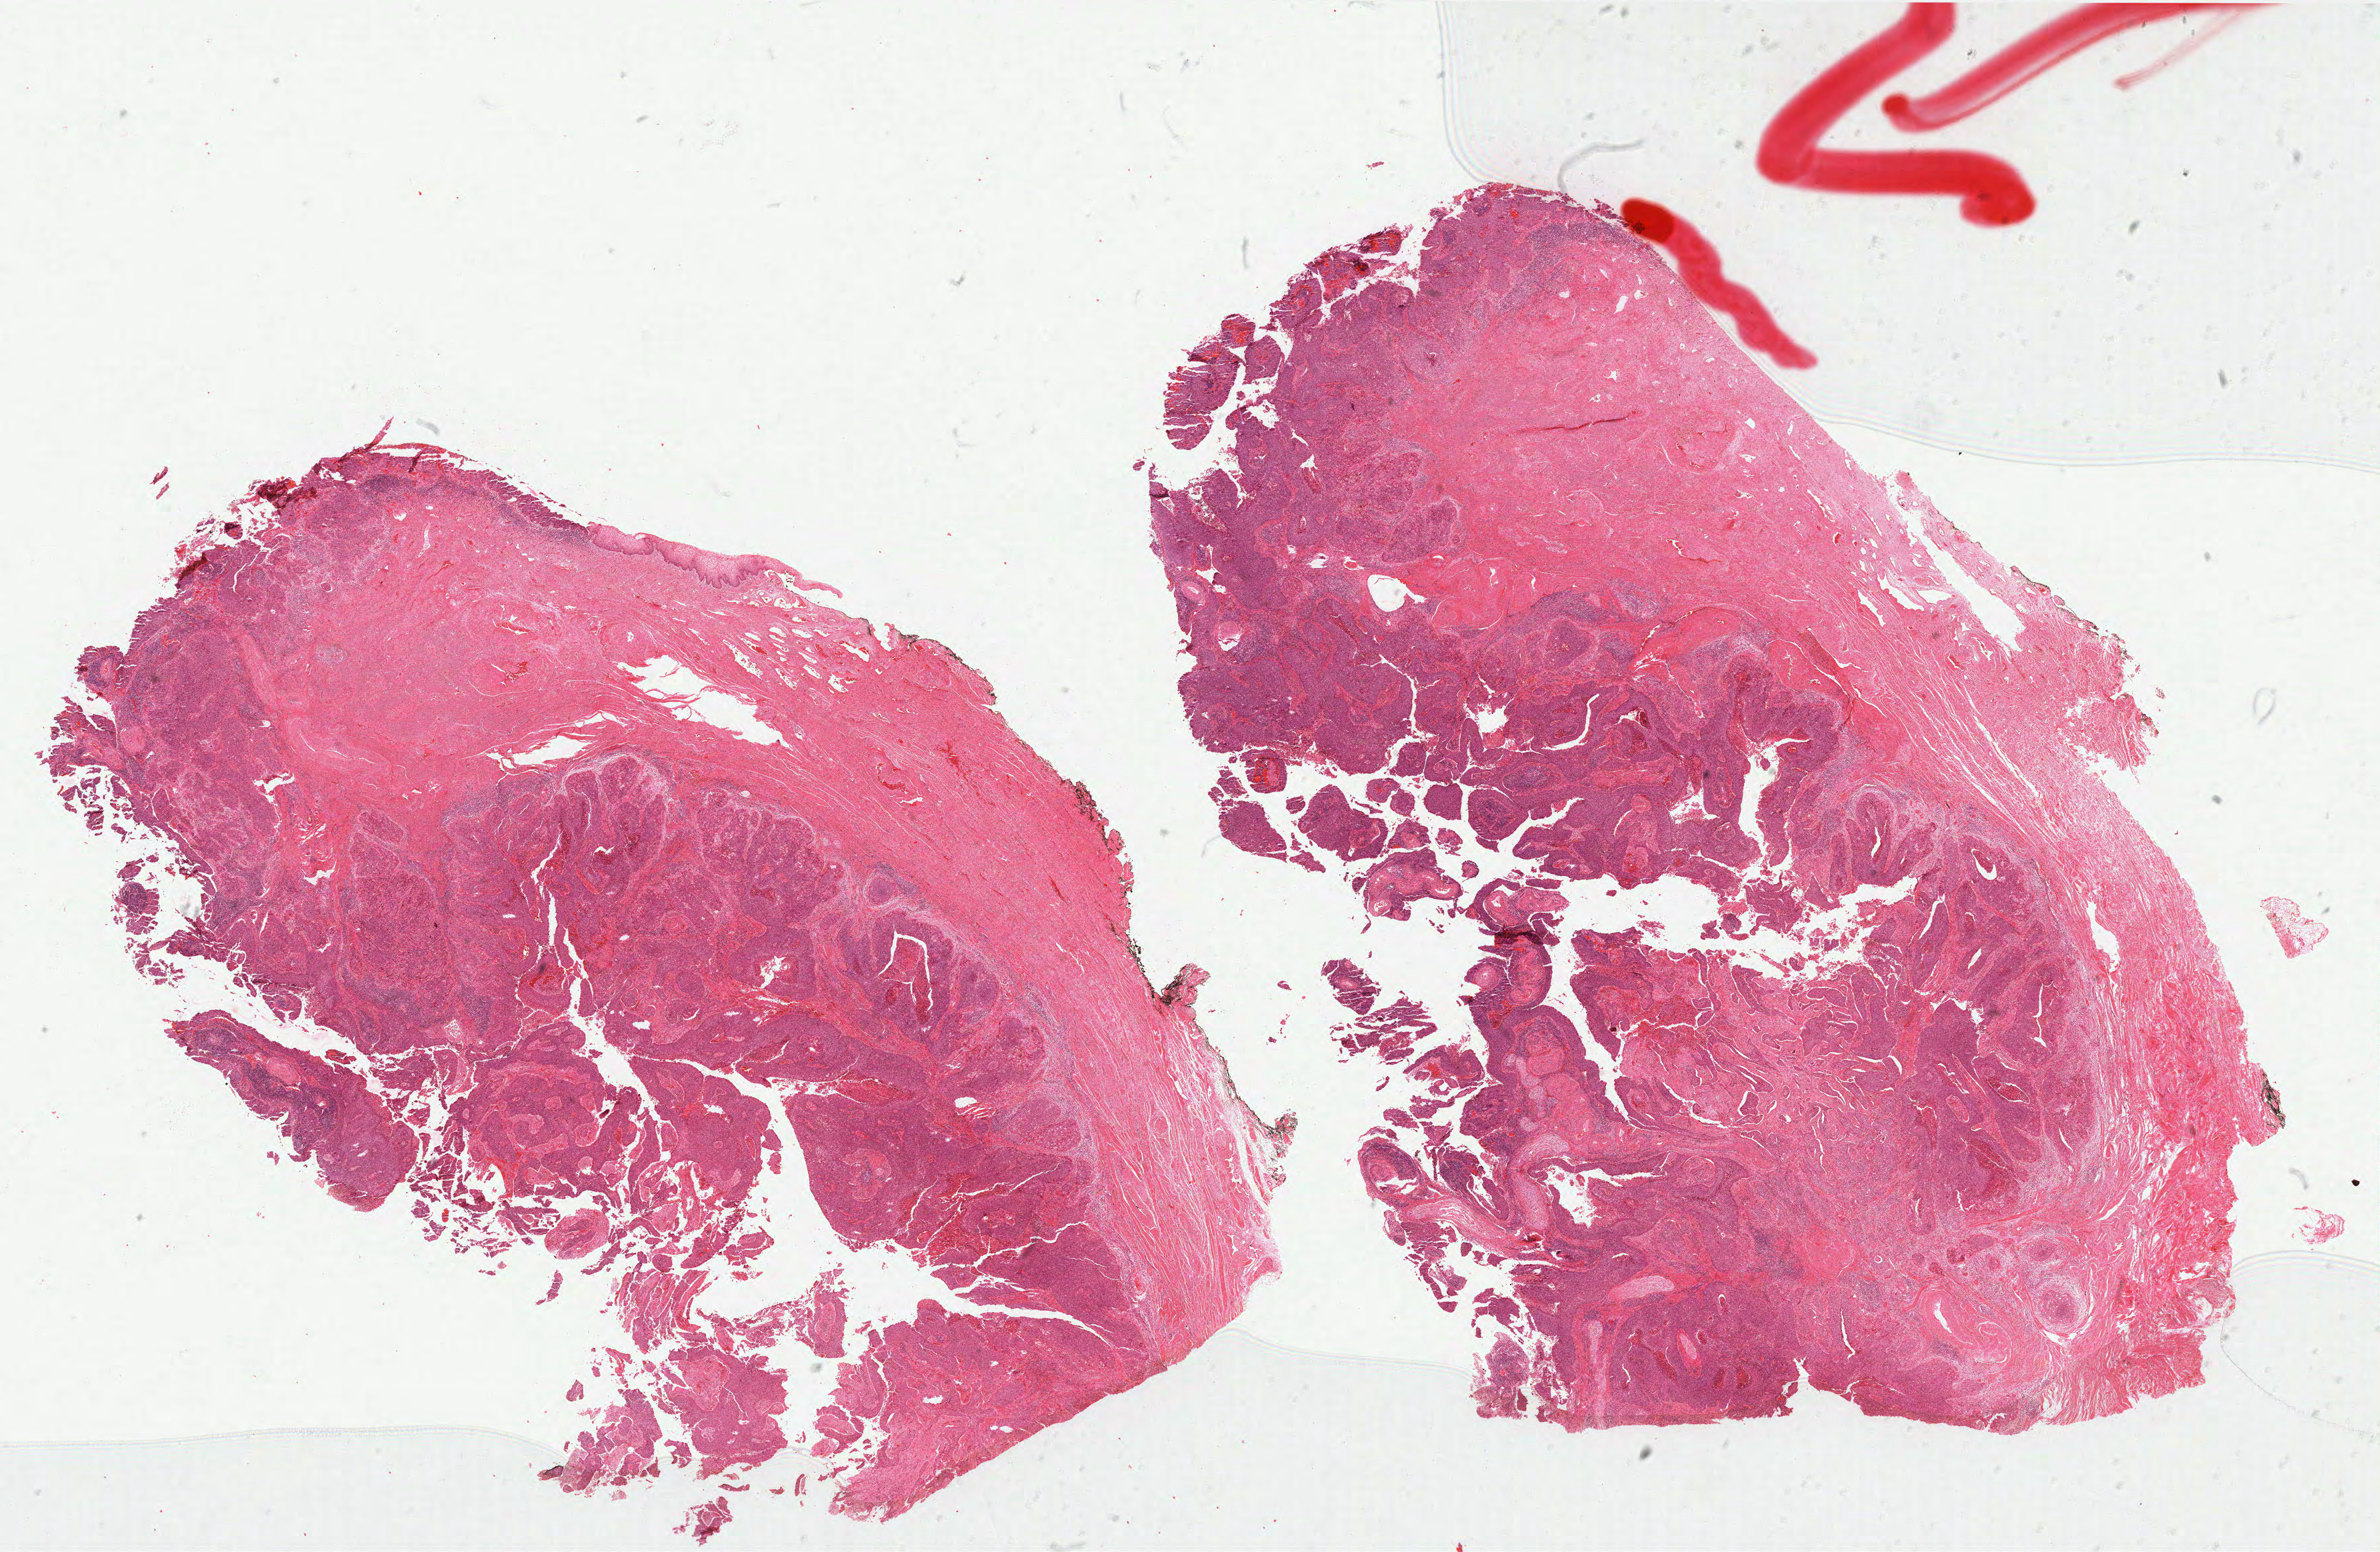
H&E whole-slide image — shown as a low-resolution overview of the whole scanned area (about 28.6 x 18.6 mm); formalin-fixed paraffin-embedded (FFPE) diagnostic section; primary tumour sample from the cervix. Female, age 37 years at initial diagnosis. Histologic grade: G2 (moderately differentiated).
* FIGO stage: IB
* lymph nodes positive (case pathology): 0 of 33 examined
* histologic diagnosis: Squamous cell carcinoma, NOS (cervix uteri)